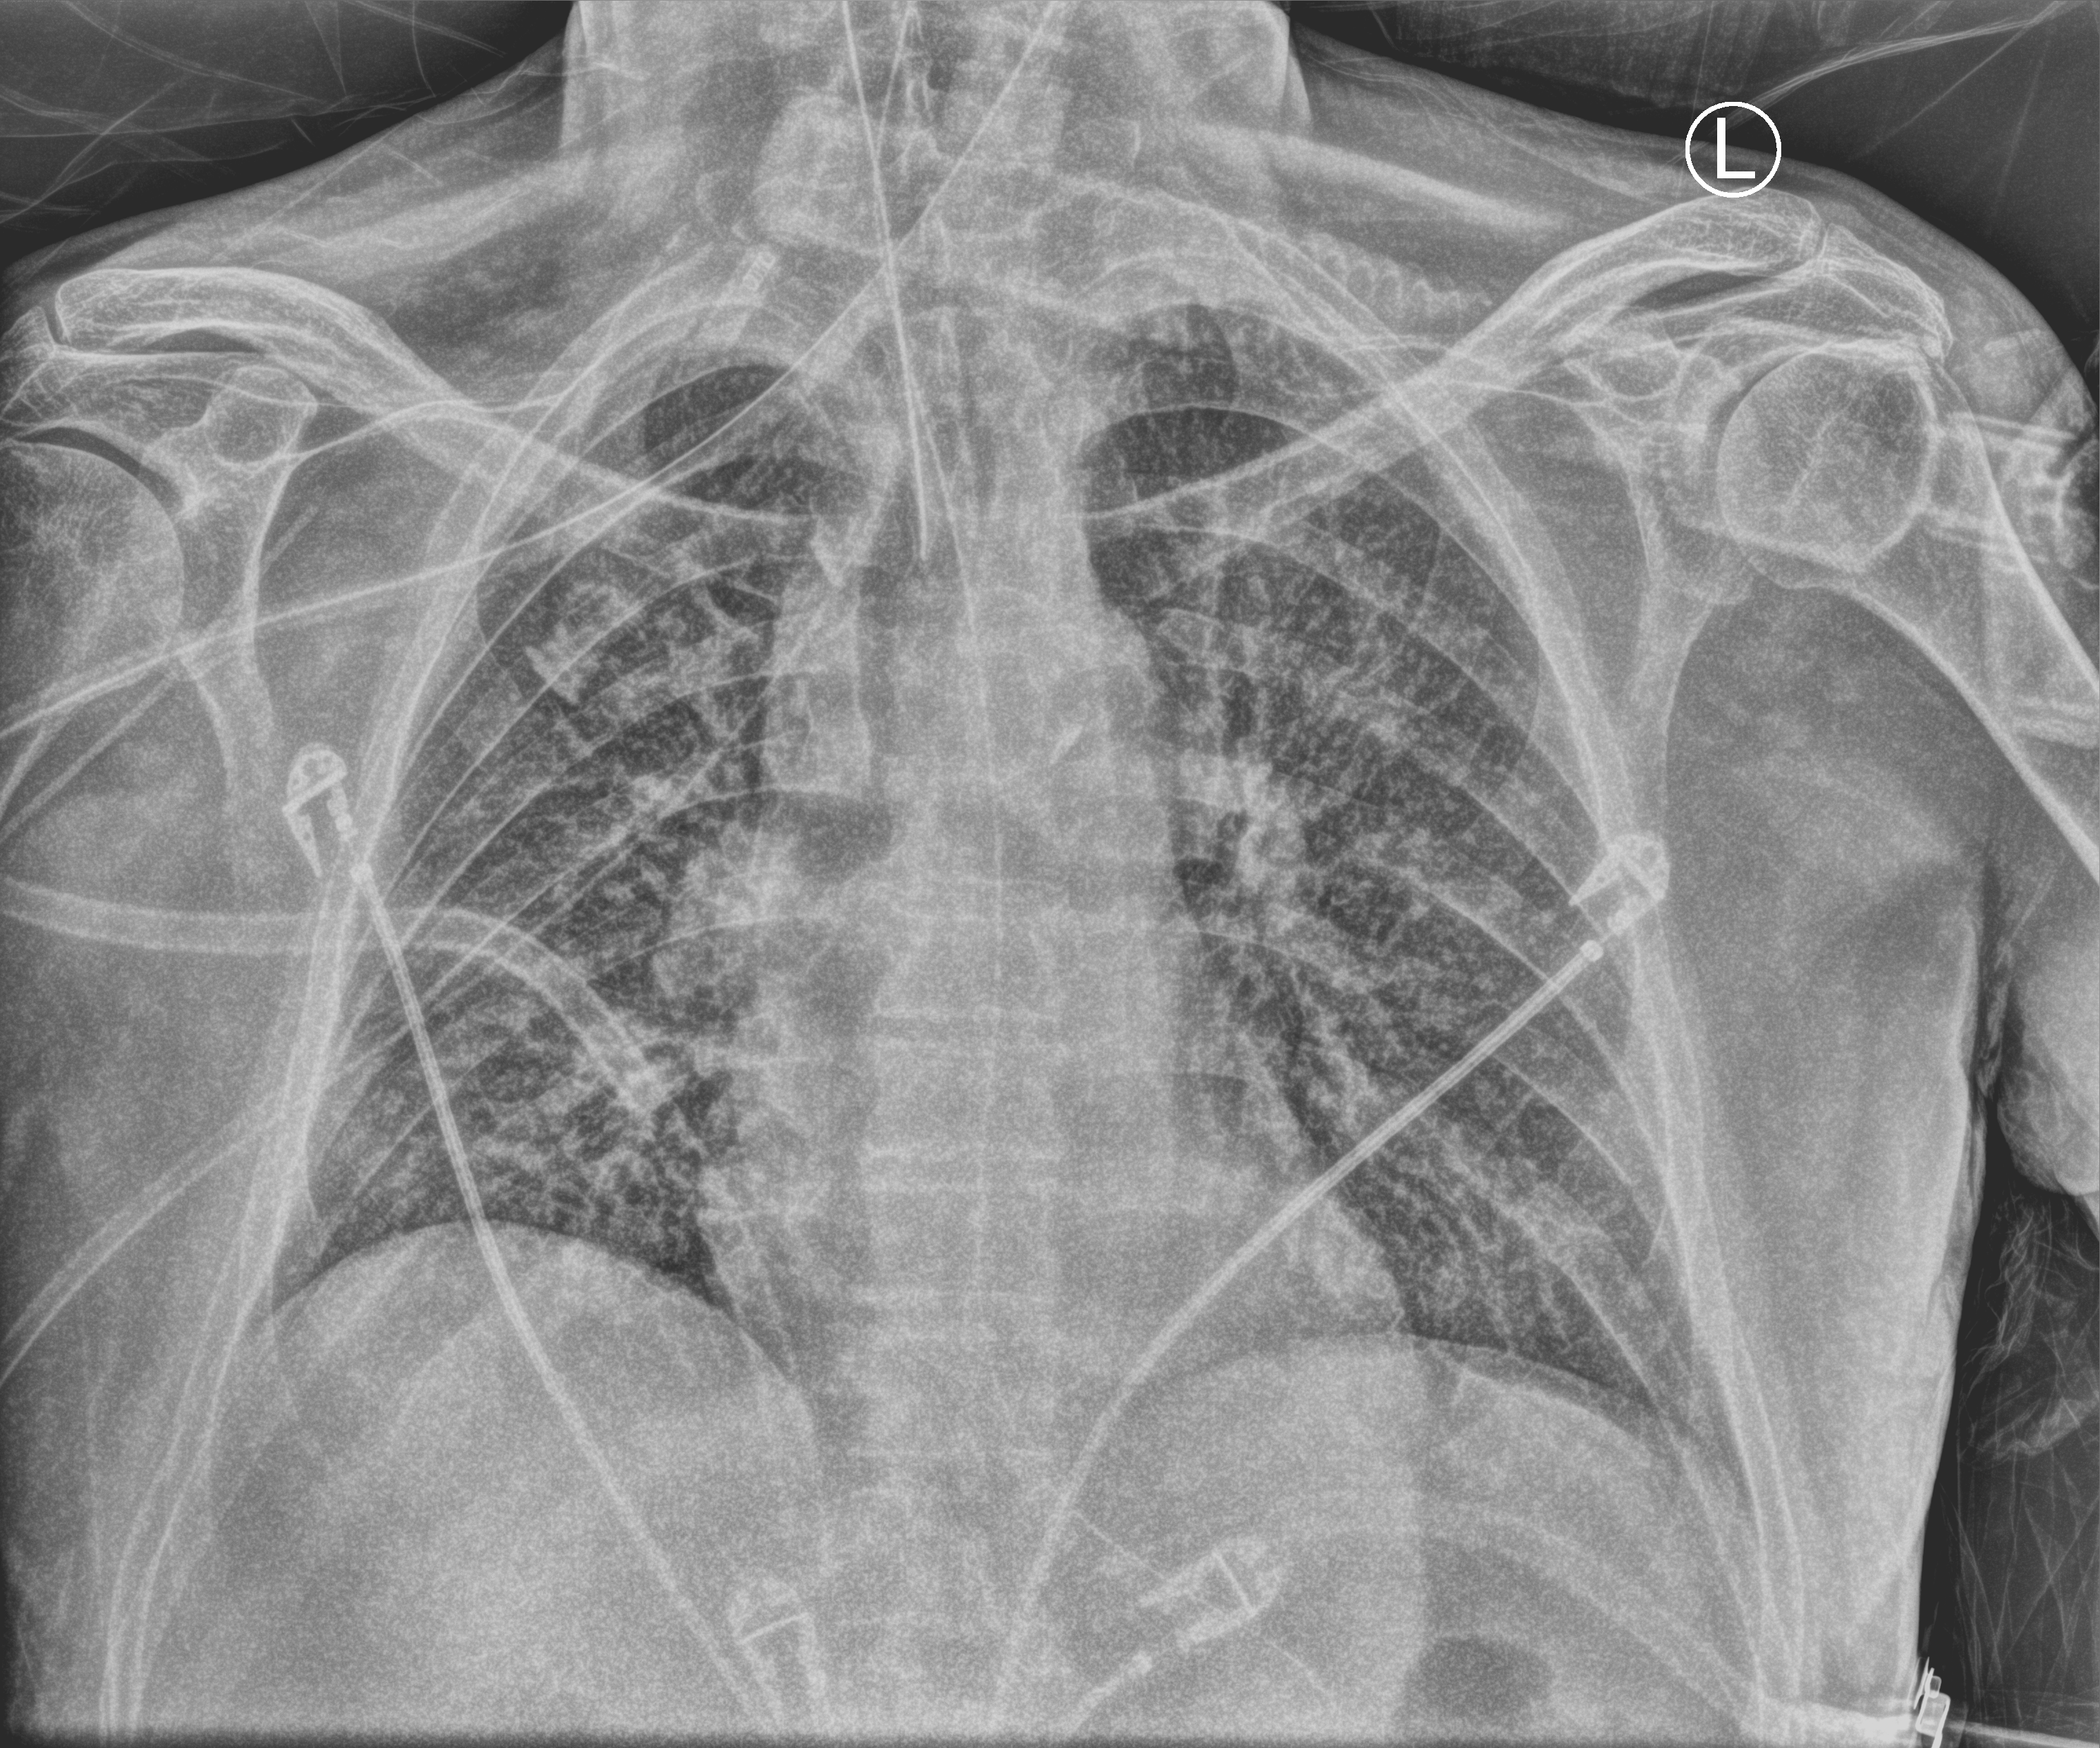
Chest X-ray (portable), anteroposterior (AP) projection. Patient hospitalised with COVID-19; male, aged 60–74 years.
From the hospital-stay record, not from the radiograph (when in the stay this image was taken is not recorded): admitted to intensive care during this hospital stay: yes.